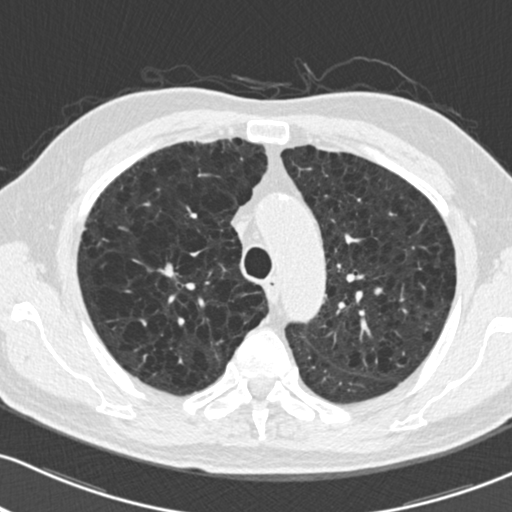
Low-dose screening chest CT, one axial slice; position 155 of 204 along the scan axis; reconstruction kernel B30f; 120 kVp; lung window (W 1500 / L -600 HU); 2 mm slice thickness; 512 × 512 image matrix.
Structures marked on this image (outlined manually by an expert reader):
- lesion 1 (tumor, upper lobe of right lung): bounding box <158,263,178,278> (left, top, right, bottom; pixels)